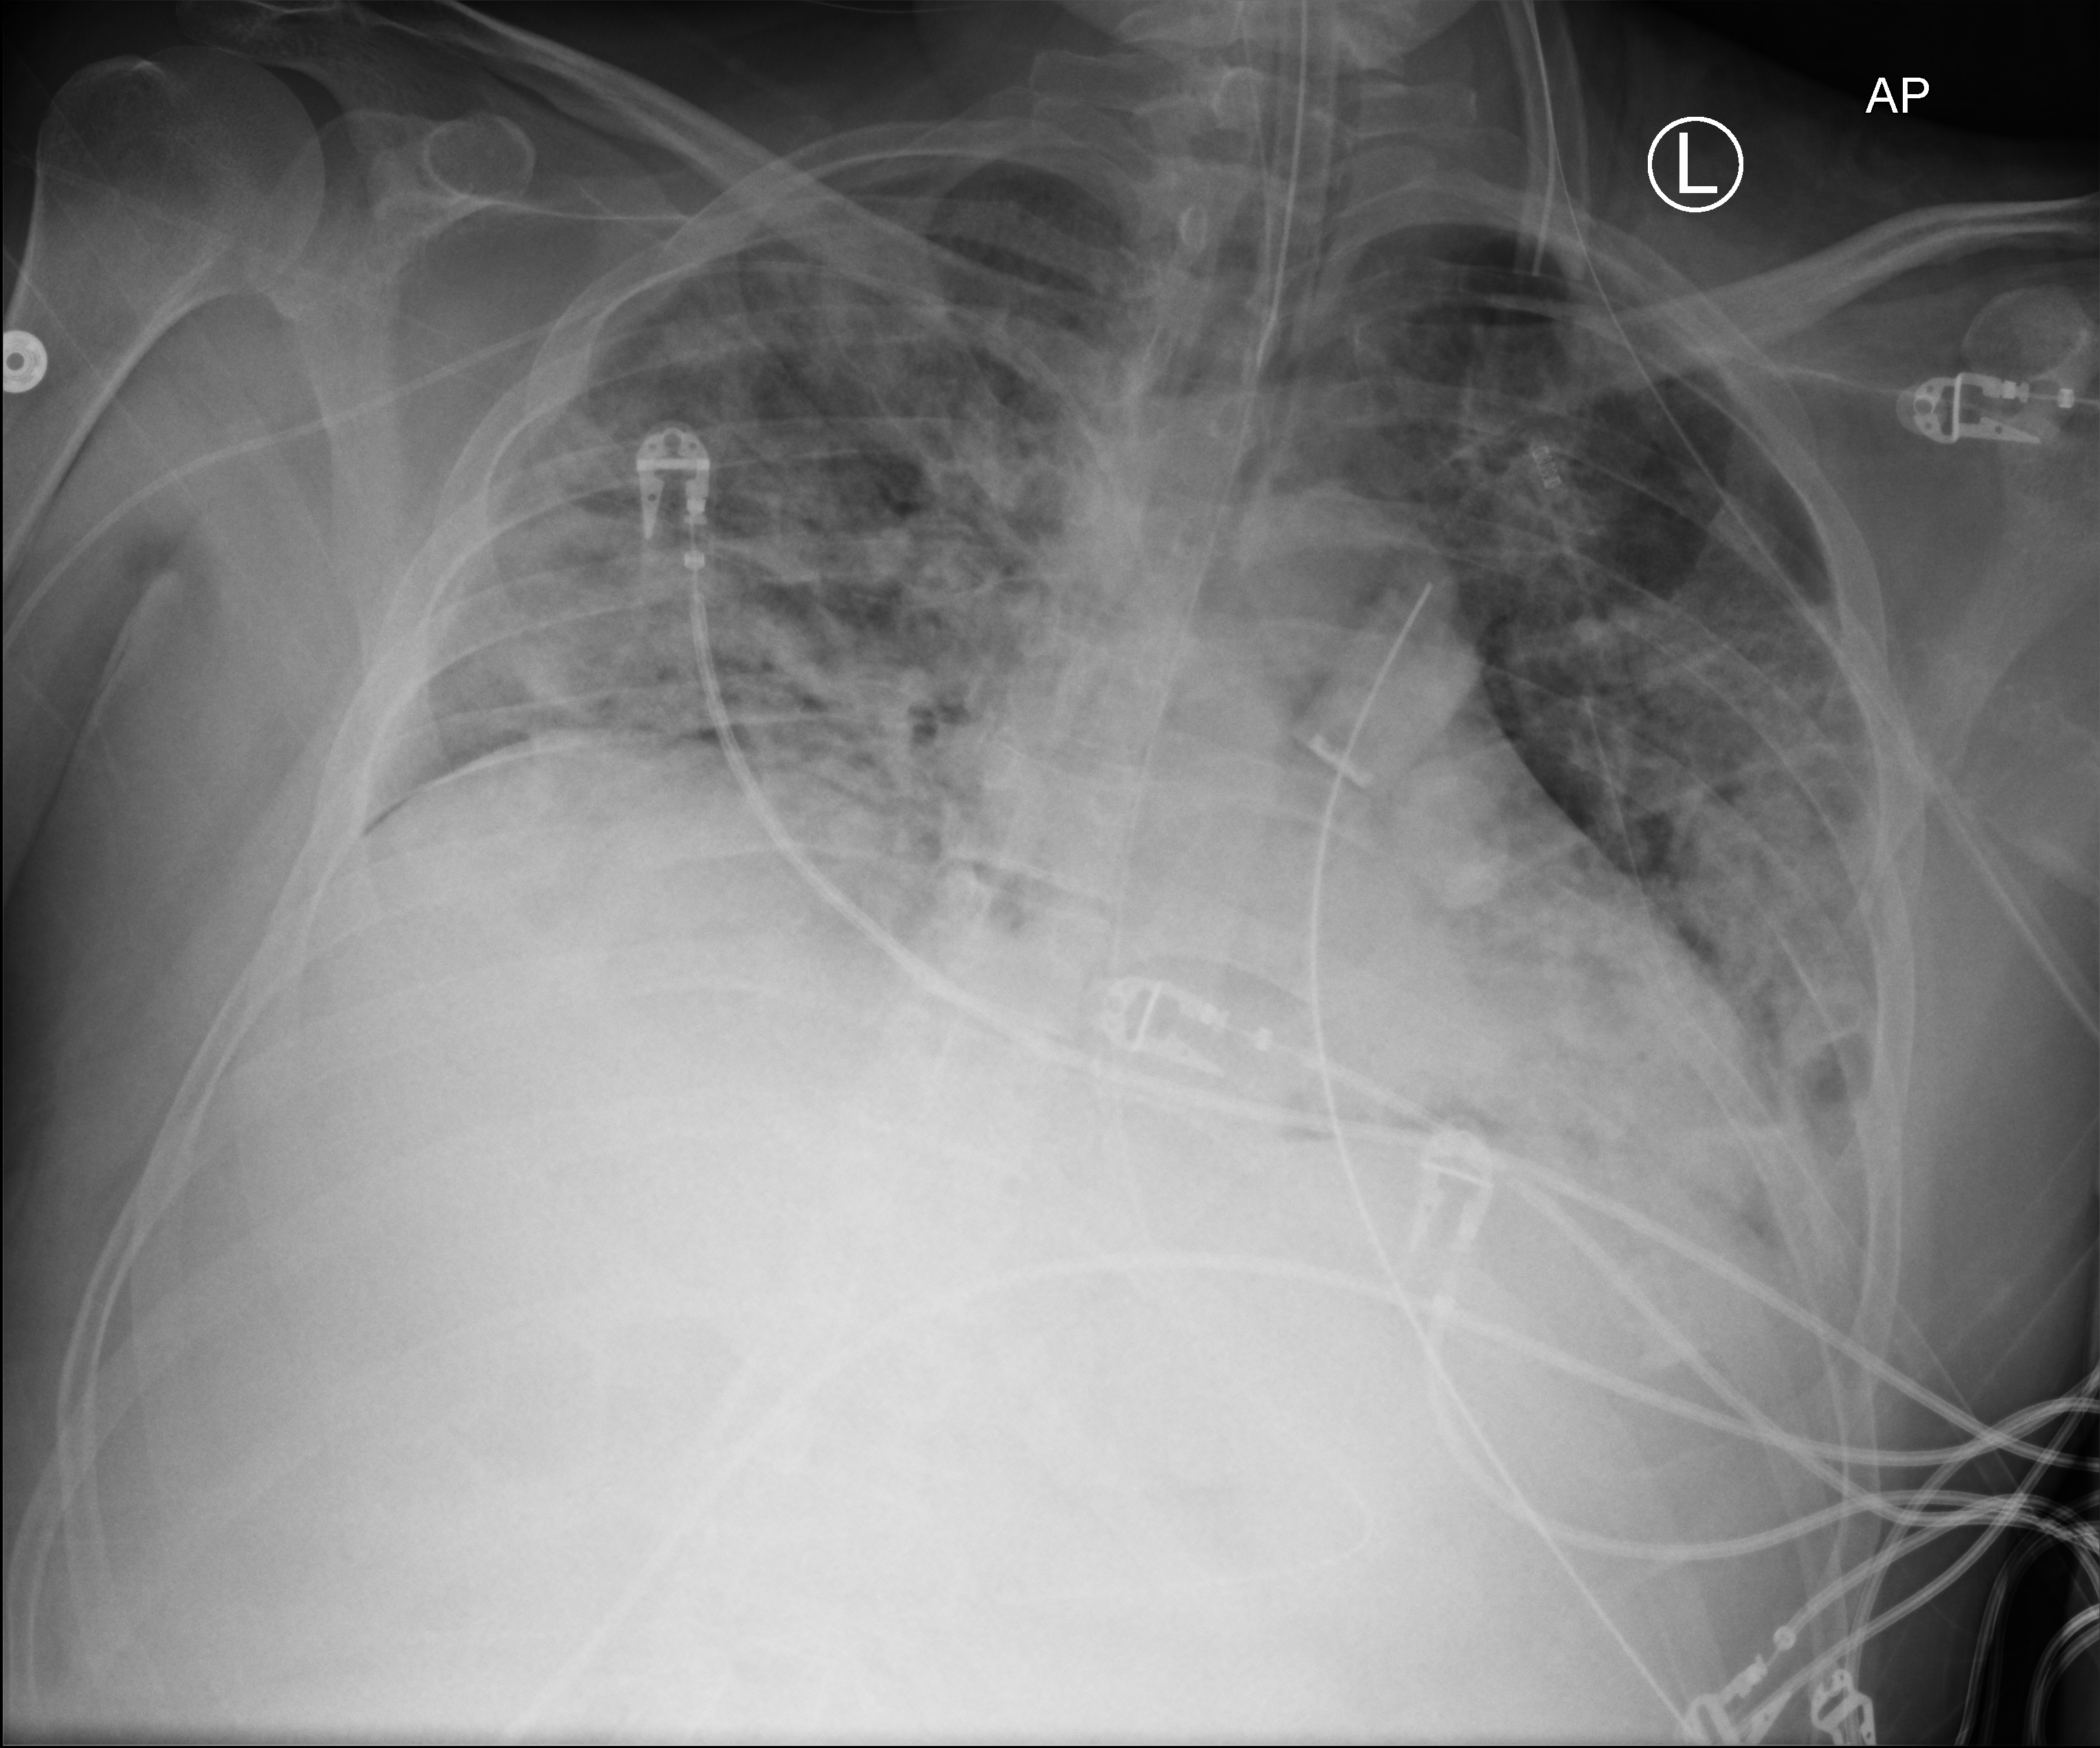
Bedside chest radiograph (computed radiography), anteroposterior (AP) projection. Male patient hospitalised with COVID-19, age 18–59 years.
From the hospital-stay record, not from the radiograph (when in the stay this image was taken is not recorded):
- length of hospital stay: 48 days
- mechanically ventilated during this hospital stay: yes
- other chronic lung disease (admission record): no